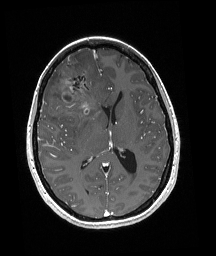
Brain MRI from a brain-tumour surgery series, one axial slice; position 91 of 192 along the scan axis; T1-weighted post-contrast; 1 mm slice thickness; 216 × 256 image matrix. Case-level facts recorded for this patient, not image findings: histopathology: Oligodendroglioma; WHO grade: 3; IDH mutation: yes; tumour location: Right Frontal.
Outlined on this slice (manually delineated by an expert):
- tumour: box from (x=51, y=62) to (x=101, y=120) px